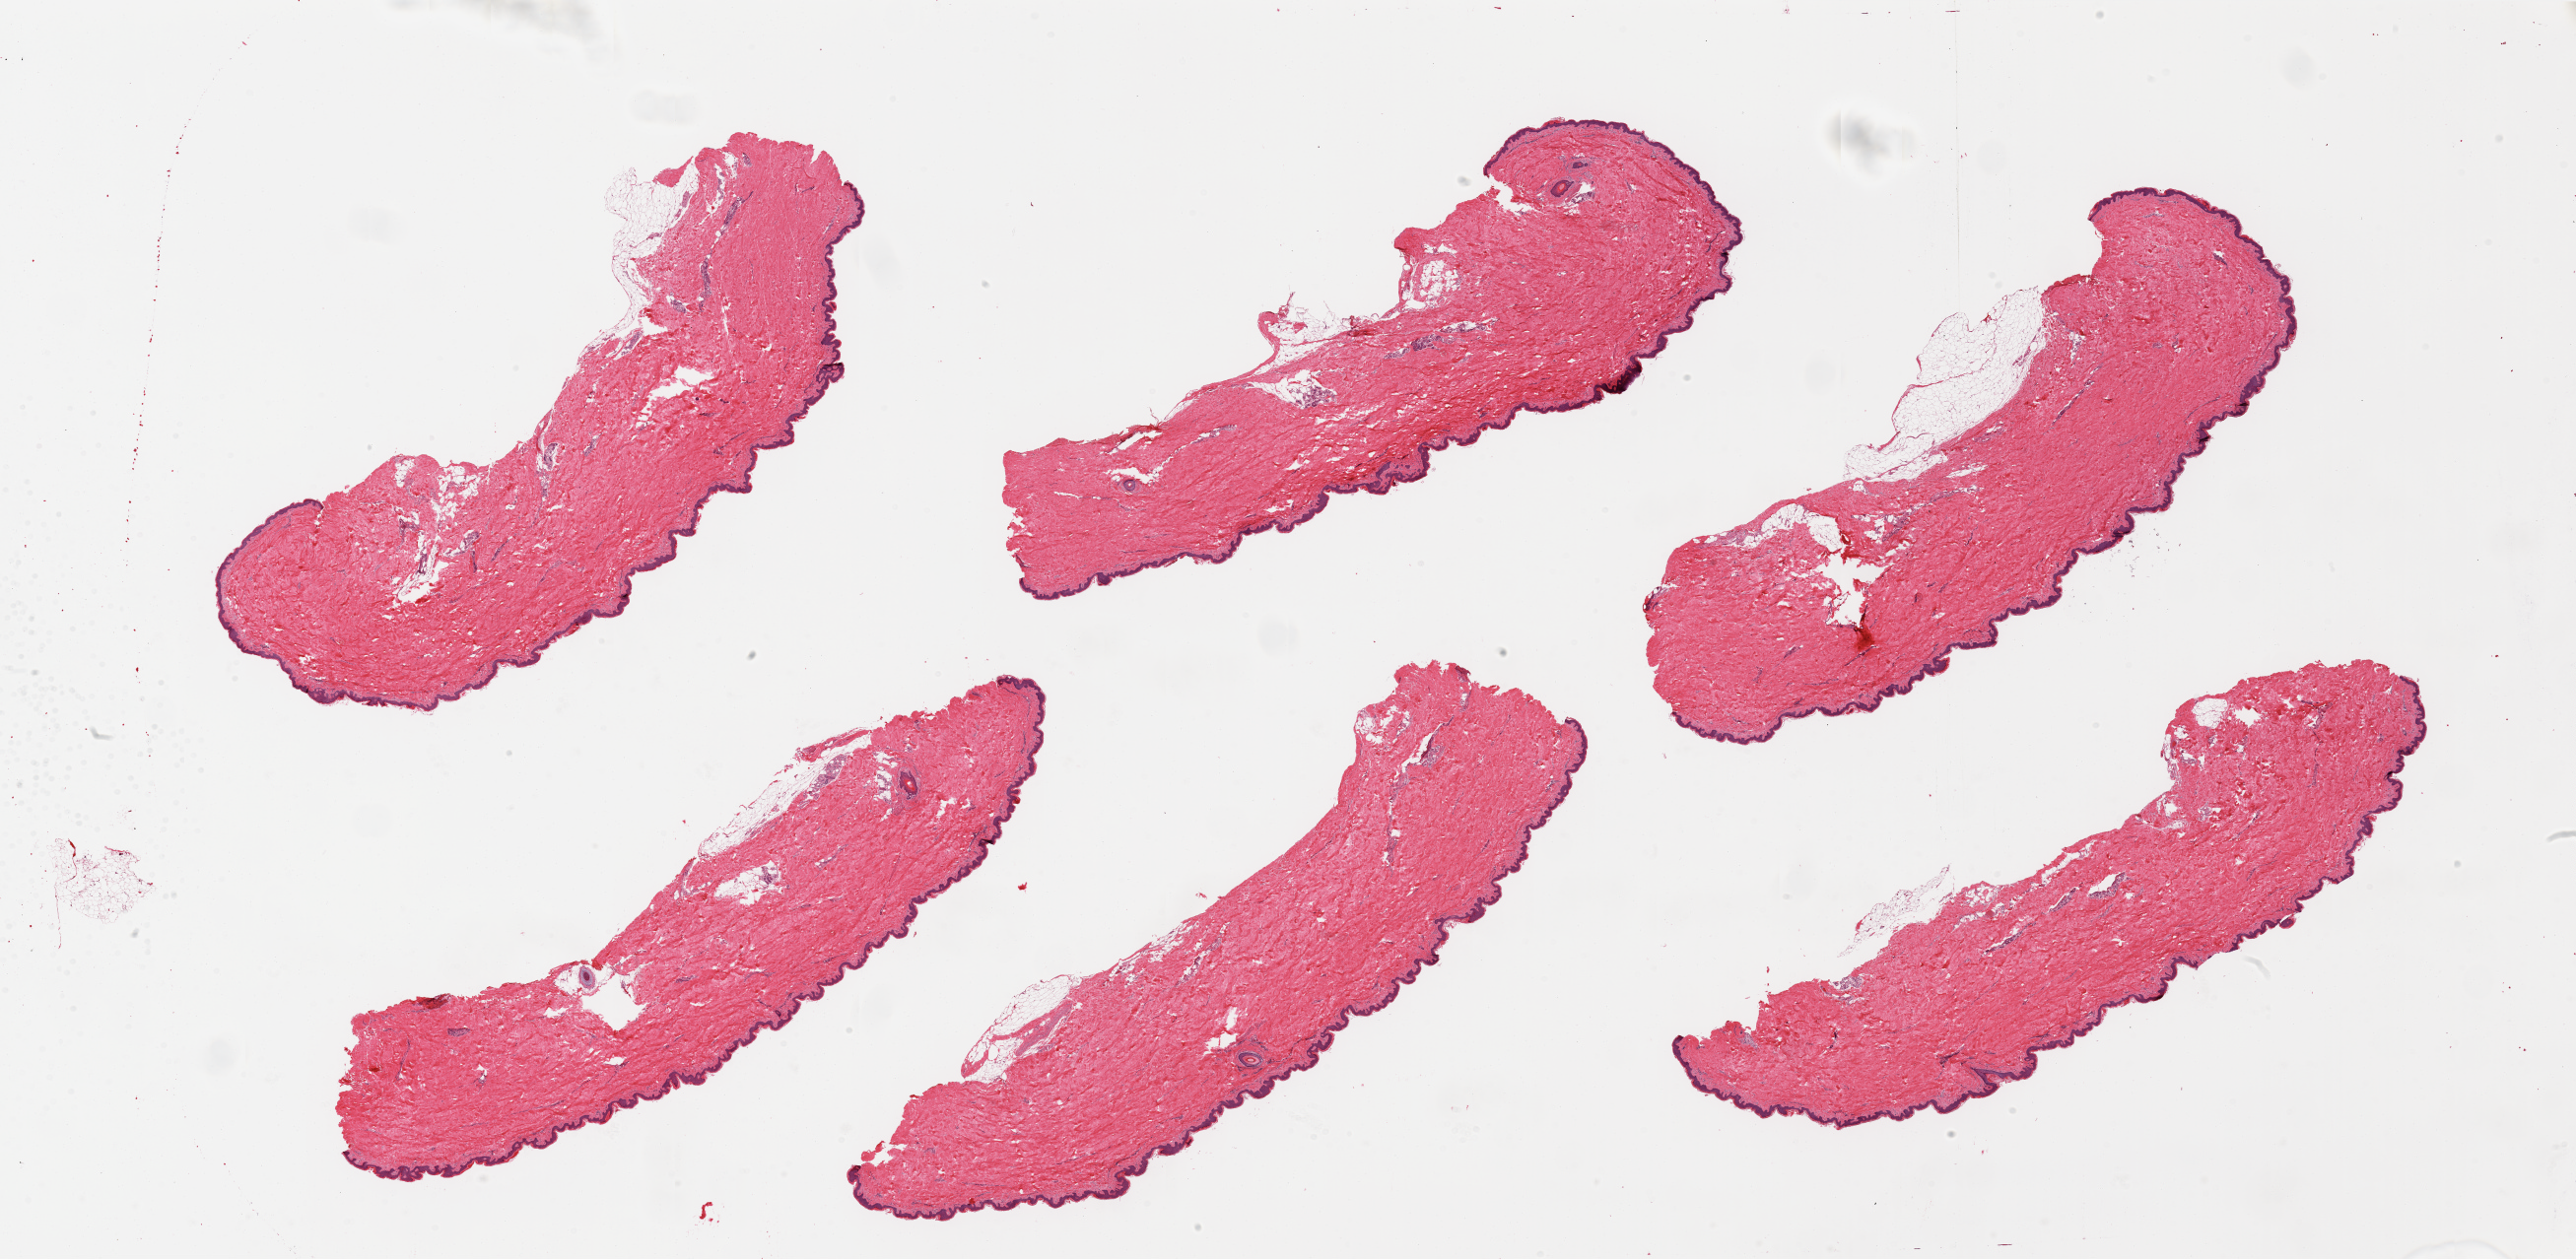
Hematoxylin and eosin (H&E) whole-slide image, brightfield — whole scanned area (about 41.3 x 20.2 mm) shown as a low-resolution overview; PAXgene-fixed, paraffin-embedded tissue; section of skin of suprapubic region (target tissue); donor tissue sample. Donor: male.
Review note (as recorded): 6 pieces; well trimmed; <5% intradermal fat.